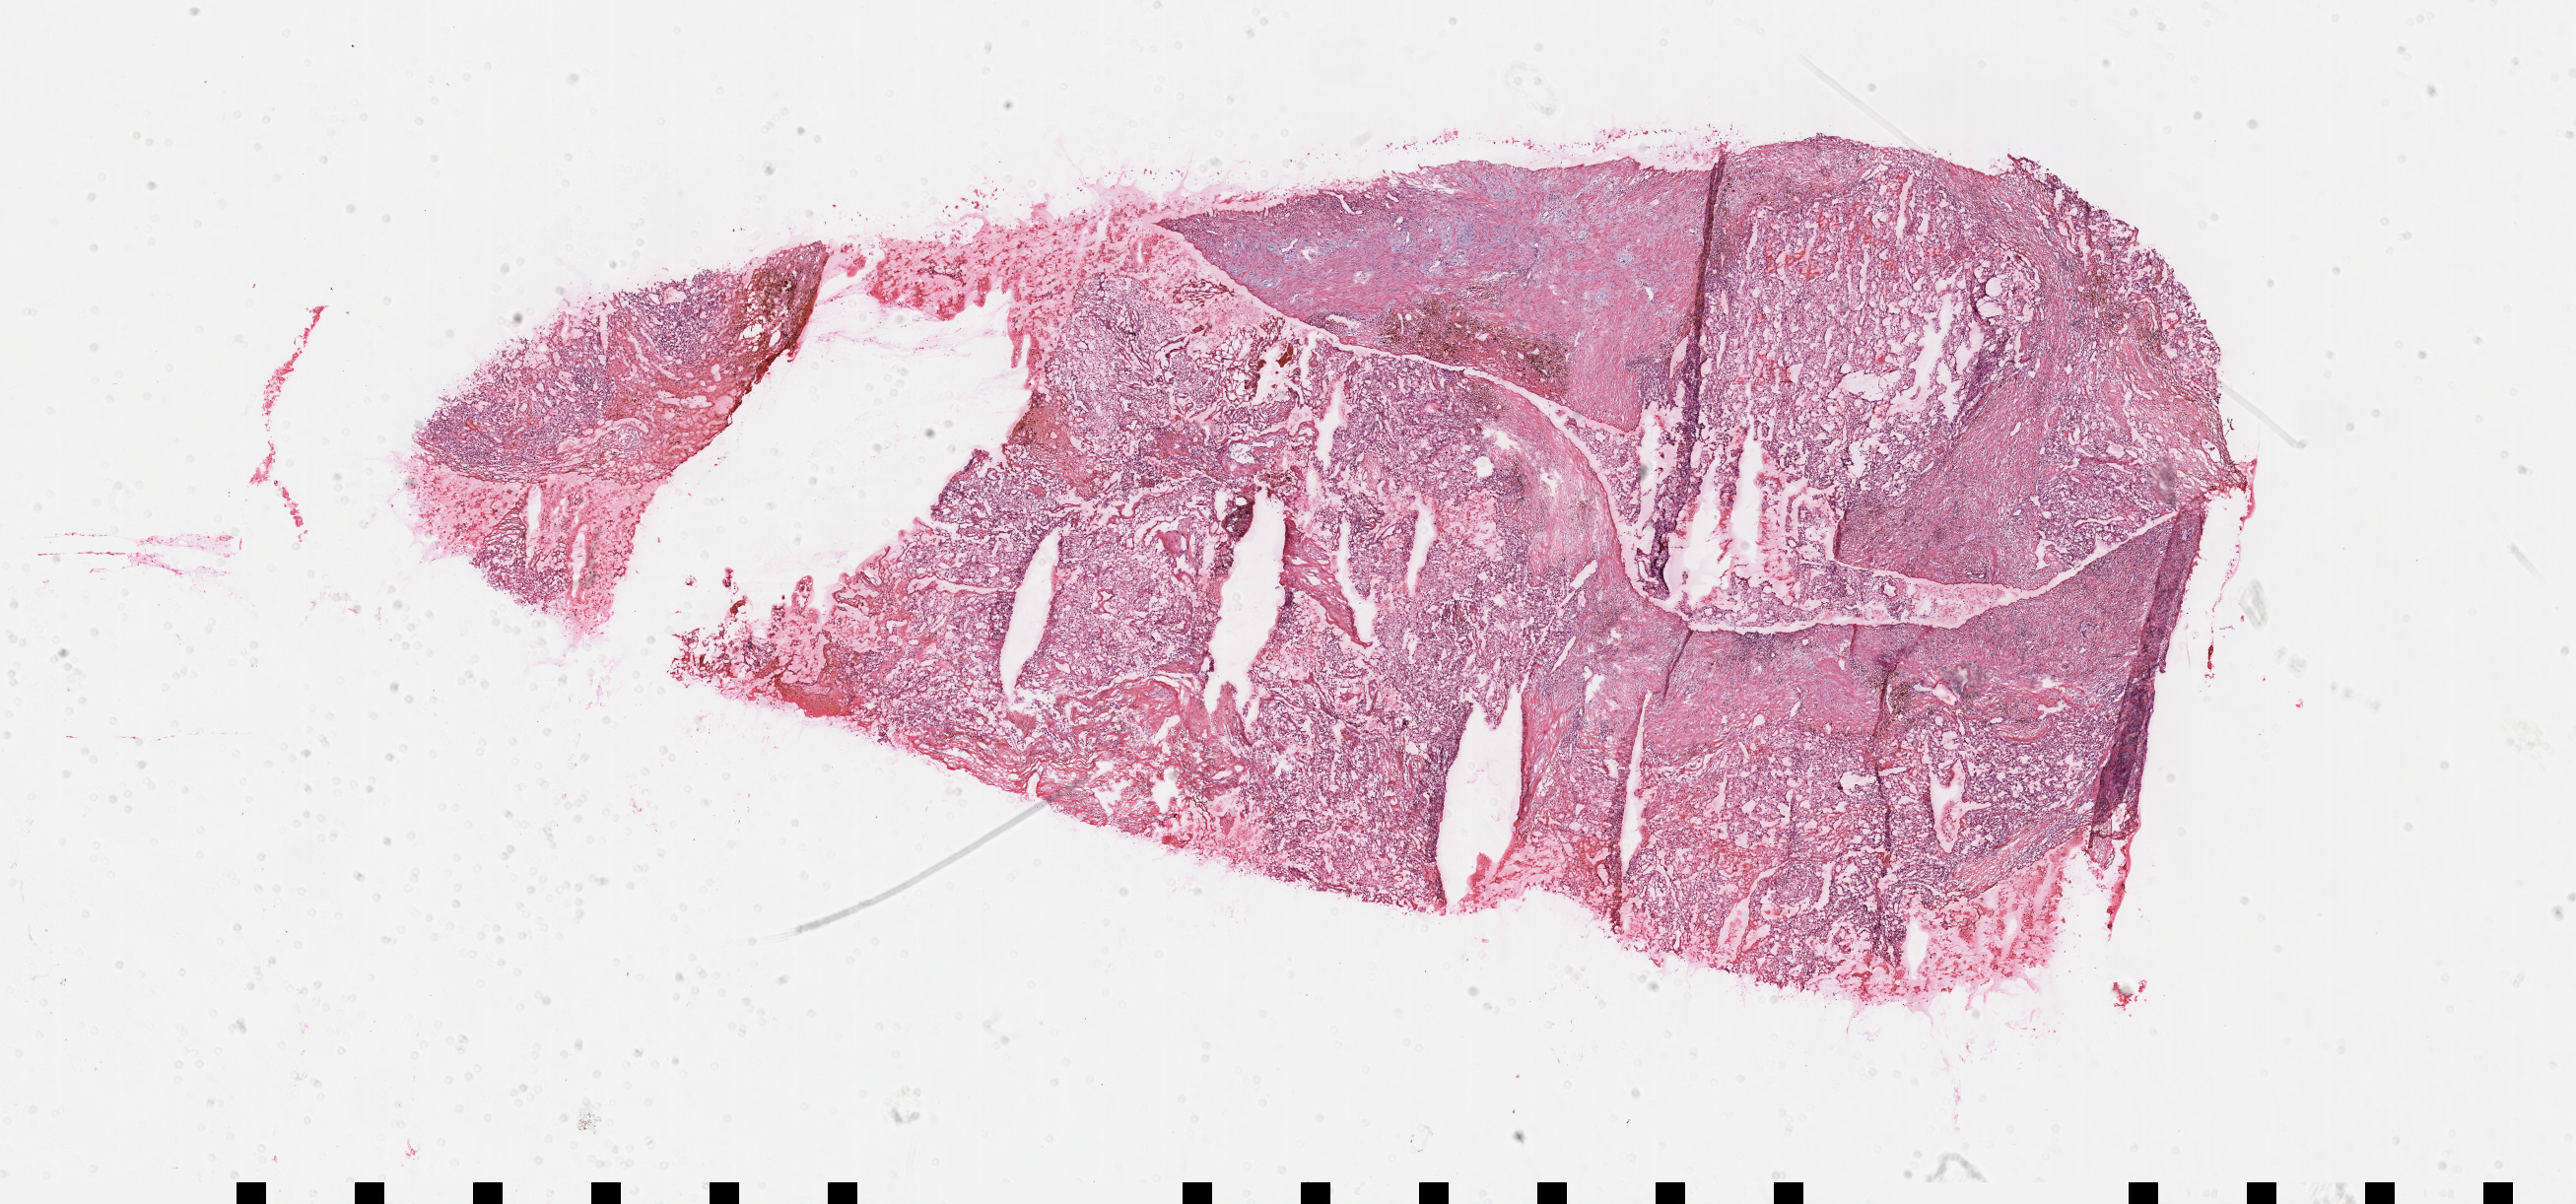
H&E whole-slide image — low-resolution overview of the scanned area, about 21.1 x 9.9 mm (acquisition: 40x scan). FFPE section. Sample: primary tumour, kidney. Male patient; age at initial diagnosis 51 years. Histologic grade: G3 (poorly differentiated).
AJCC pathologic stage: I (7th edition). Diagnosis: Clear cell adenocarcinoma, NOS.